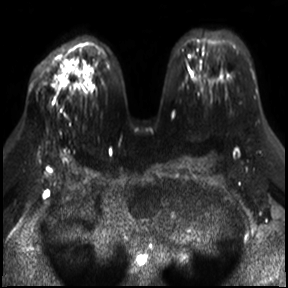
Breast MRI, one axial slice. Slice 19 of 30 in the series (ordered by position). Diffusion-weighted series; image 2 of 4 stored at this slice position (different b-values; order by instance number). 3 T. 4 mm slice thickness. 288 × 288 image matrix, field of view 340 × 340 mm. Female patient.
Annotated regions visible in this slice (outlined manually by an expert reader):
- tumour on diffusion-weighted imaging: bounding box [x1, y1, x2, y2] px = [60, 80, 66, 85]